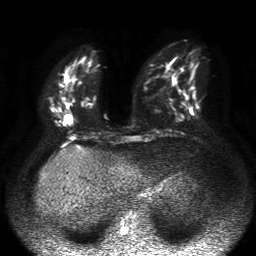
Breast MRI, one axial slice. Diffusion-weighted series; image 2 of 4 stored at this slice position (different b-values; order by instance number). 1.5 T. 256 × 256 image matrix. Female patient.
Annotated regions visible in this slice (outlined manually by an expert reader):
- tumour on diffusion-weighted imaging: bounding box (x1, y1, x2, y2) in pixels: (63, 113, 73, 125)